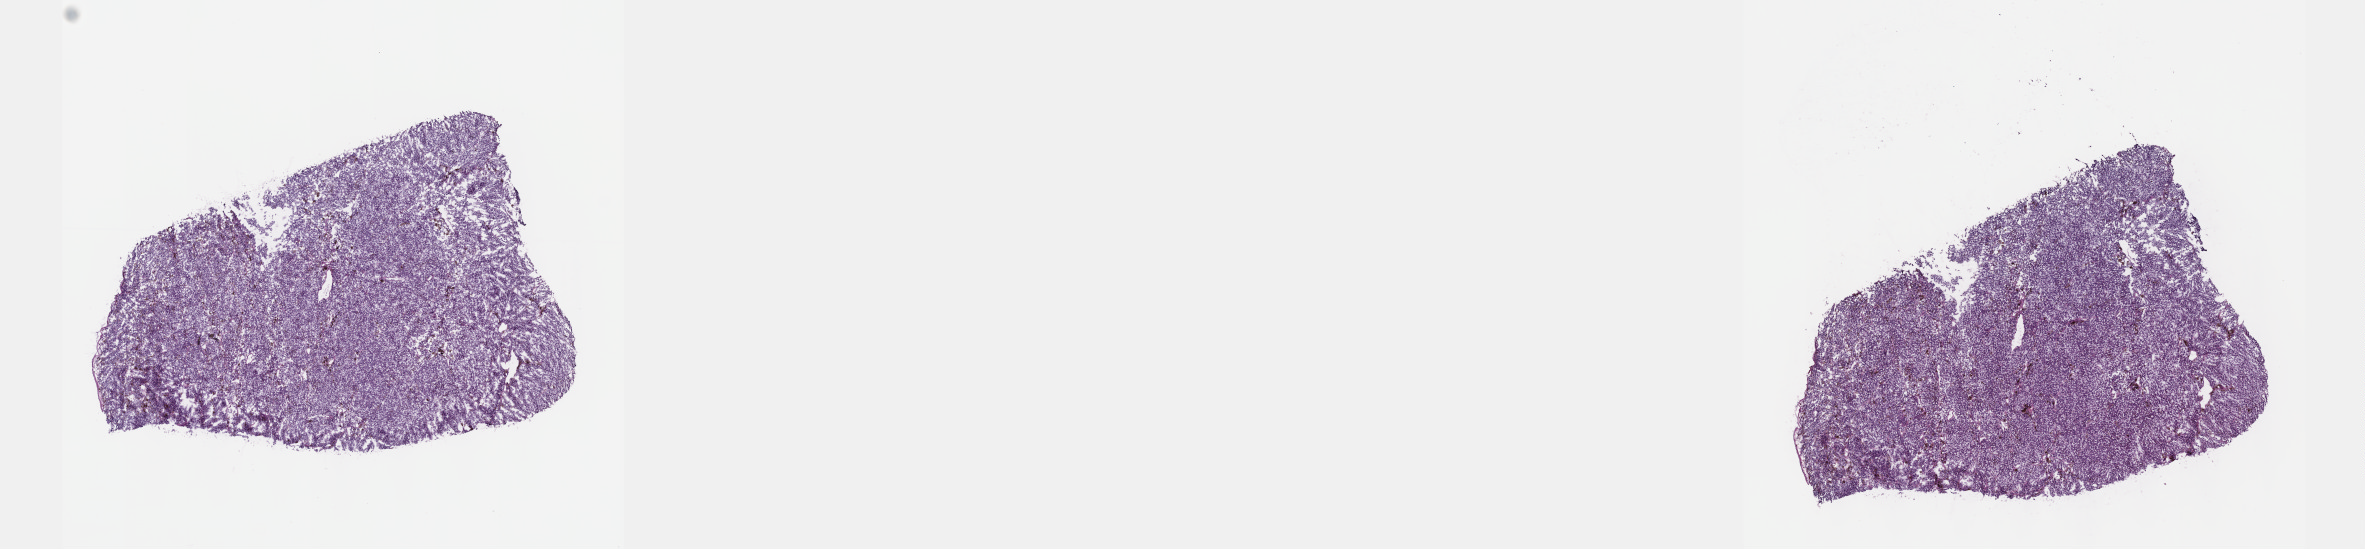
Whole-slide histology image, Hematoxylin and eosin (H&E) stained, a low-resolution overview of the entire scanned area, about 19.1 x 4.4 mm (acquisition: 40x scan). Frozen section from the top of the tissue portion. Uvea, primary tumour sample. Female, age 83 years at initial diagnosis.
Pathologic diagnosis: Spindle cell melanoma, NOS (overlapping lesion of eye and adnexa).